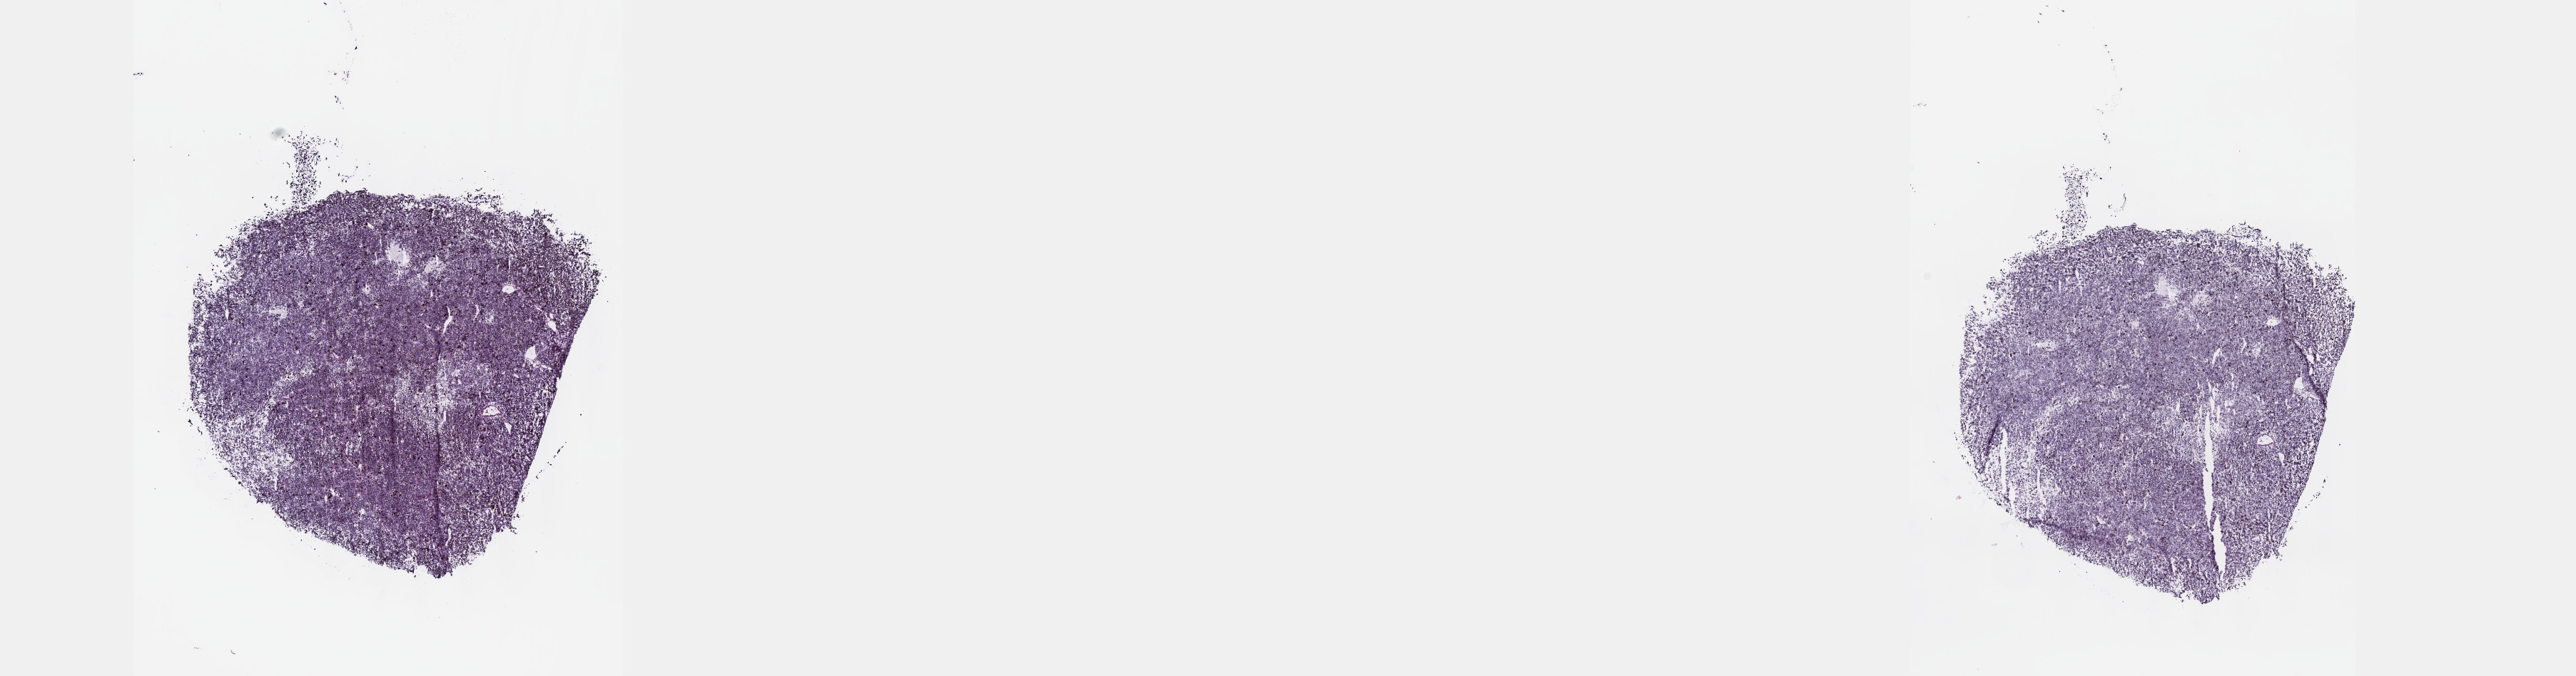
Hematoxylin and eosin (H&E) stained whole-slide image — whole scanned area (about 29.2 x 7.7 mm, slide scanned at 40x) shown as a low-resolution overview. Frozen section from the top of the tissue portion. Uvea, primary tumour sample. Male, age 49 years at initial diagnosis. Pathologist review of this section (percent, as recorded): tumour cells 100%, tumour nuclei 80%, normal cells 0%, stromal cells 0%, necrosis 0%. Inflammatory infiltration, as recorded: lymphocyte infiltration 2%, monocyte infiltration 0%, neutrophil infiltration 0%.
AJCC pathologic stage: IIIA. Diagnosis: Epithelioid cell melanoma (choroid).